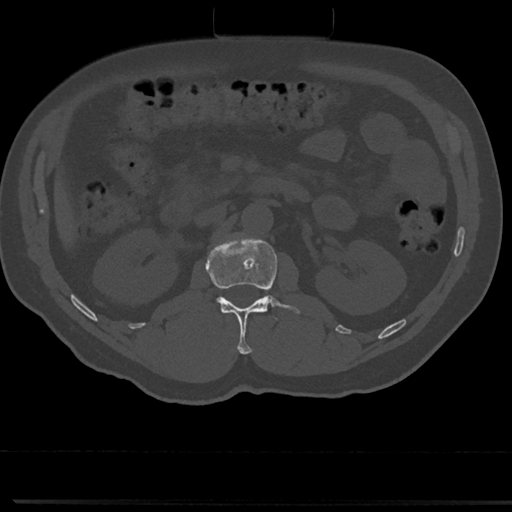
CT including the spine, one axial slice; slice 70 of 817 in the series (ordered by position); reconstruction kernel Br40s/3; bone window (W 1800 / L 400 HU); 0.5 mm slice thickness; 512 × 512 image matrix, field of view 355 × 355 mm. Male patient, age 61 years. From the clinical record (not read from this slice): primary cancer: prostate.
Outlined on this slice (semi-automatic segmentation, software-assisted and operator-edited):
- L1 vertebra: box from (x=207, y=235) to (x=302, y=354) px